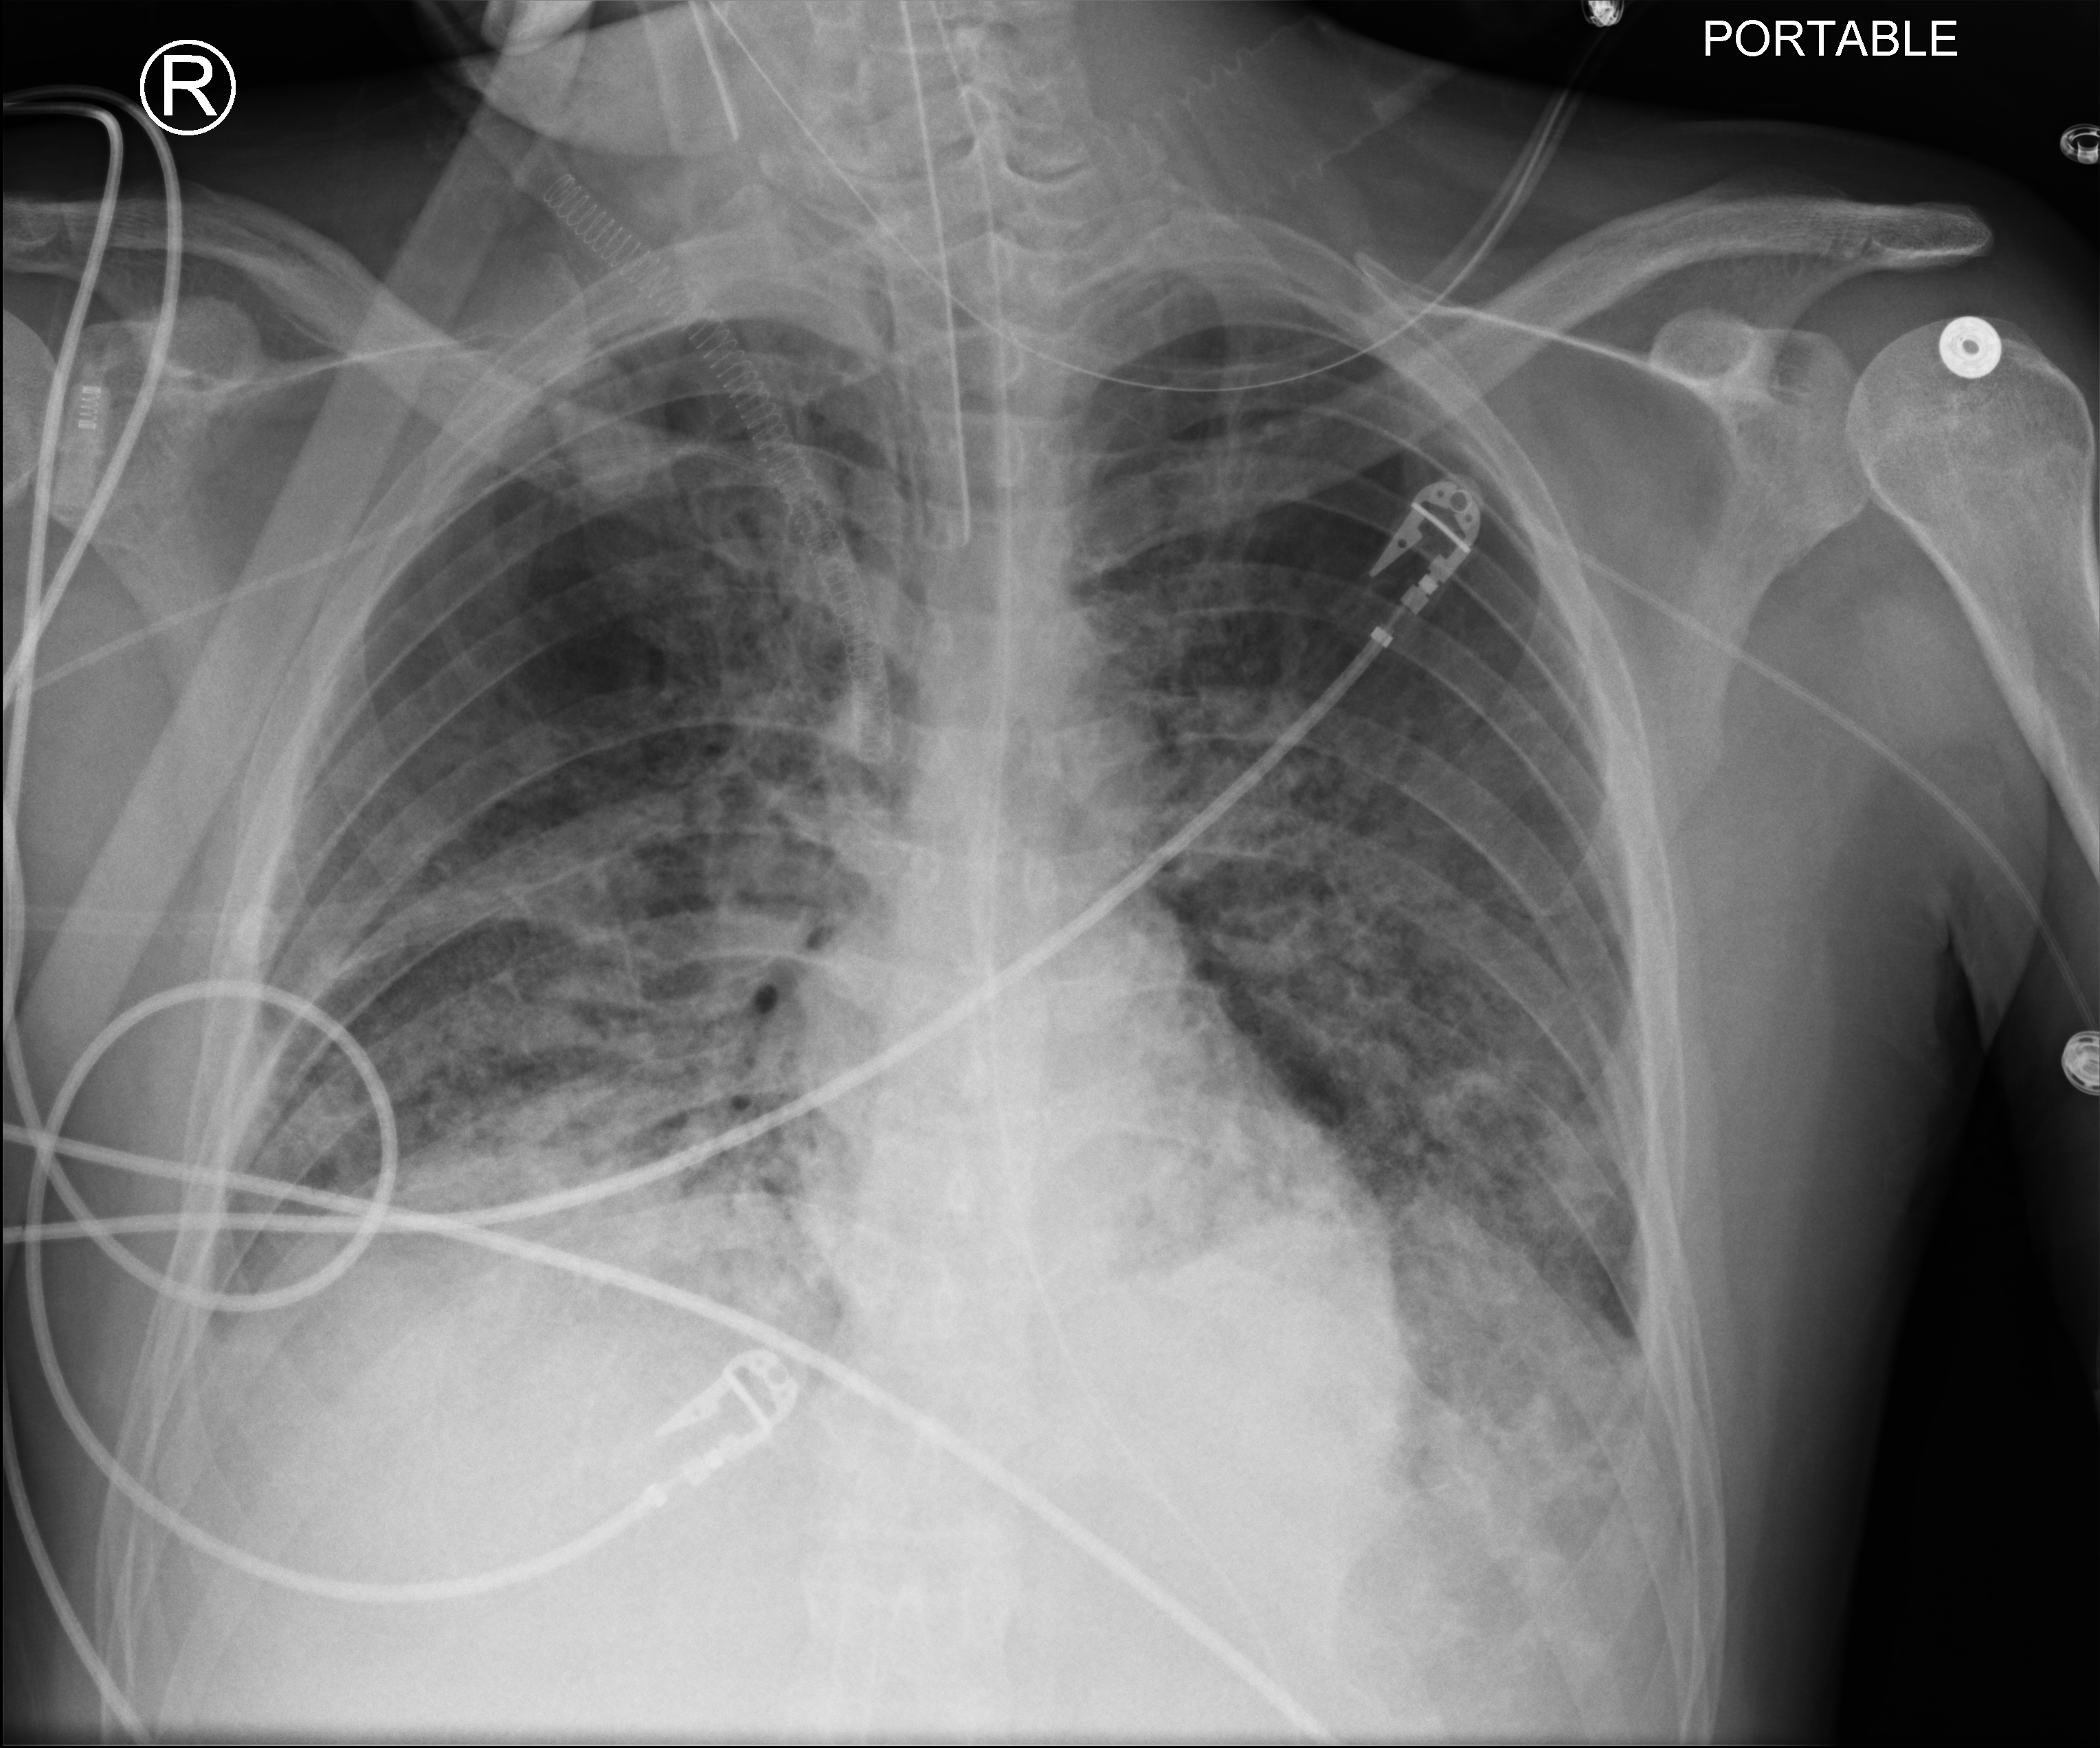
Chest X-ray (portable), anteroposterior (AP) projection. Adult patient hospitalised with COVID-19, age 18–59 years.
Hospital-stay facts (about this admission, not read from this image; timing relative to this image not recorded): diabetes (admission record): no.